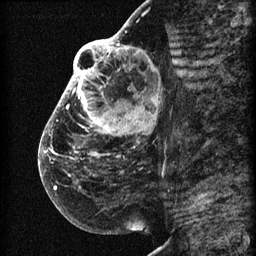
Breast MRI (dynamic contrast-enhanced), one sagittal slice. Position 33 of 60 along the scan axis. 3 images stored at this slice position (order not interpretable as contrast timing). 1.5 T. TE 4.2 ms, TR 22.7 ms. 2 mm slice thickness. 256 × 256 image matrix, field of view 180 × 180 mm. Patient: female, 48 years. From the clinical record (not read from this slice): setting: breast cancer imaged before/during neoadjuvant chemotherapy; receptor status: triple-negative.
Outlined on this slice (semi-automatically segmented with operator editing):
- analysis volume of interest (the breast-tissue region the enhancement analysis was run in; not a lesion): bounding box (x1, y1, x2, y2) in pixels: (44, 30, 173, 207)
- tumour enhancement mask (voxels above the 90 % enhancement threshold inside the analysis volume of interest): (44, 30, 155, 190)